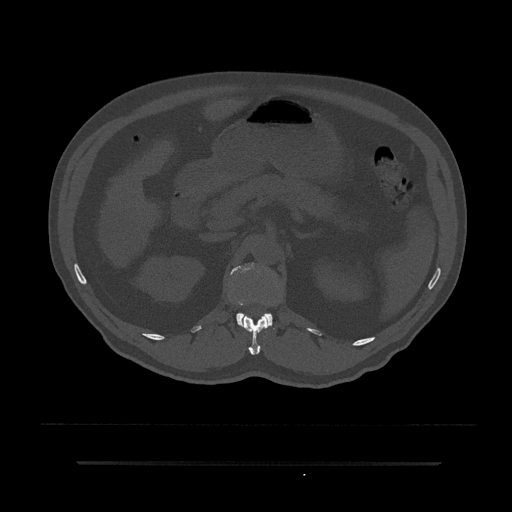
CT including the spine, one axial slice. Reconstruction kernel Br40s/3. 120 kVp. Bone window (W 1800 / L 400 HU). 0.5 mm slice thickness. 512 × 512 image matrix, field of view 464 × 464 mm. Male patient, age 59 years. From the clinical record (not read from this slice): primary cancer: bile ducts.
Outlined on this slice (semi-automatic segmentation, software-assisted and operator-edited):
- L1 vertebra: box from (x=231, y=264) to (x=273, y=326) px
- T12 vertebra: (x=241, y=314)–(x=269, y=355)